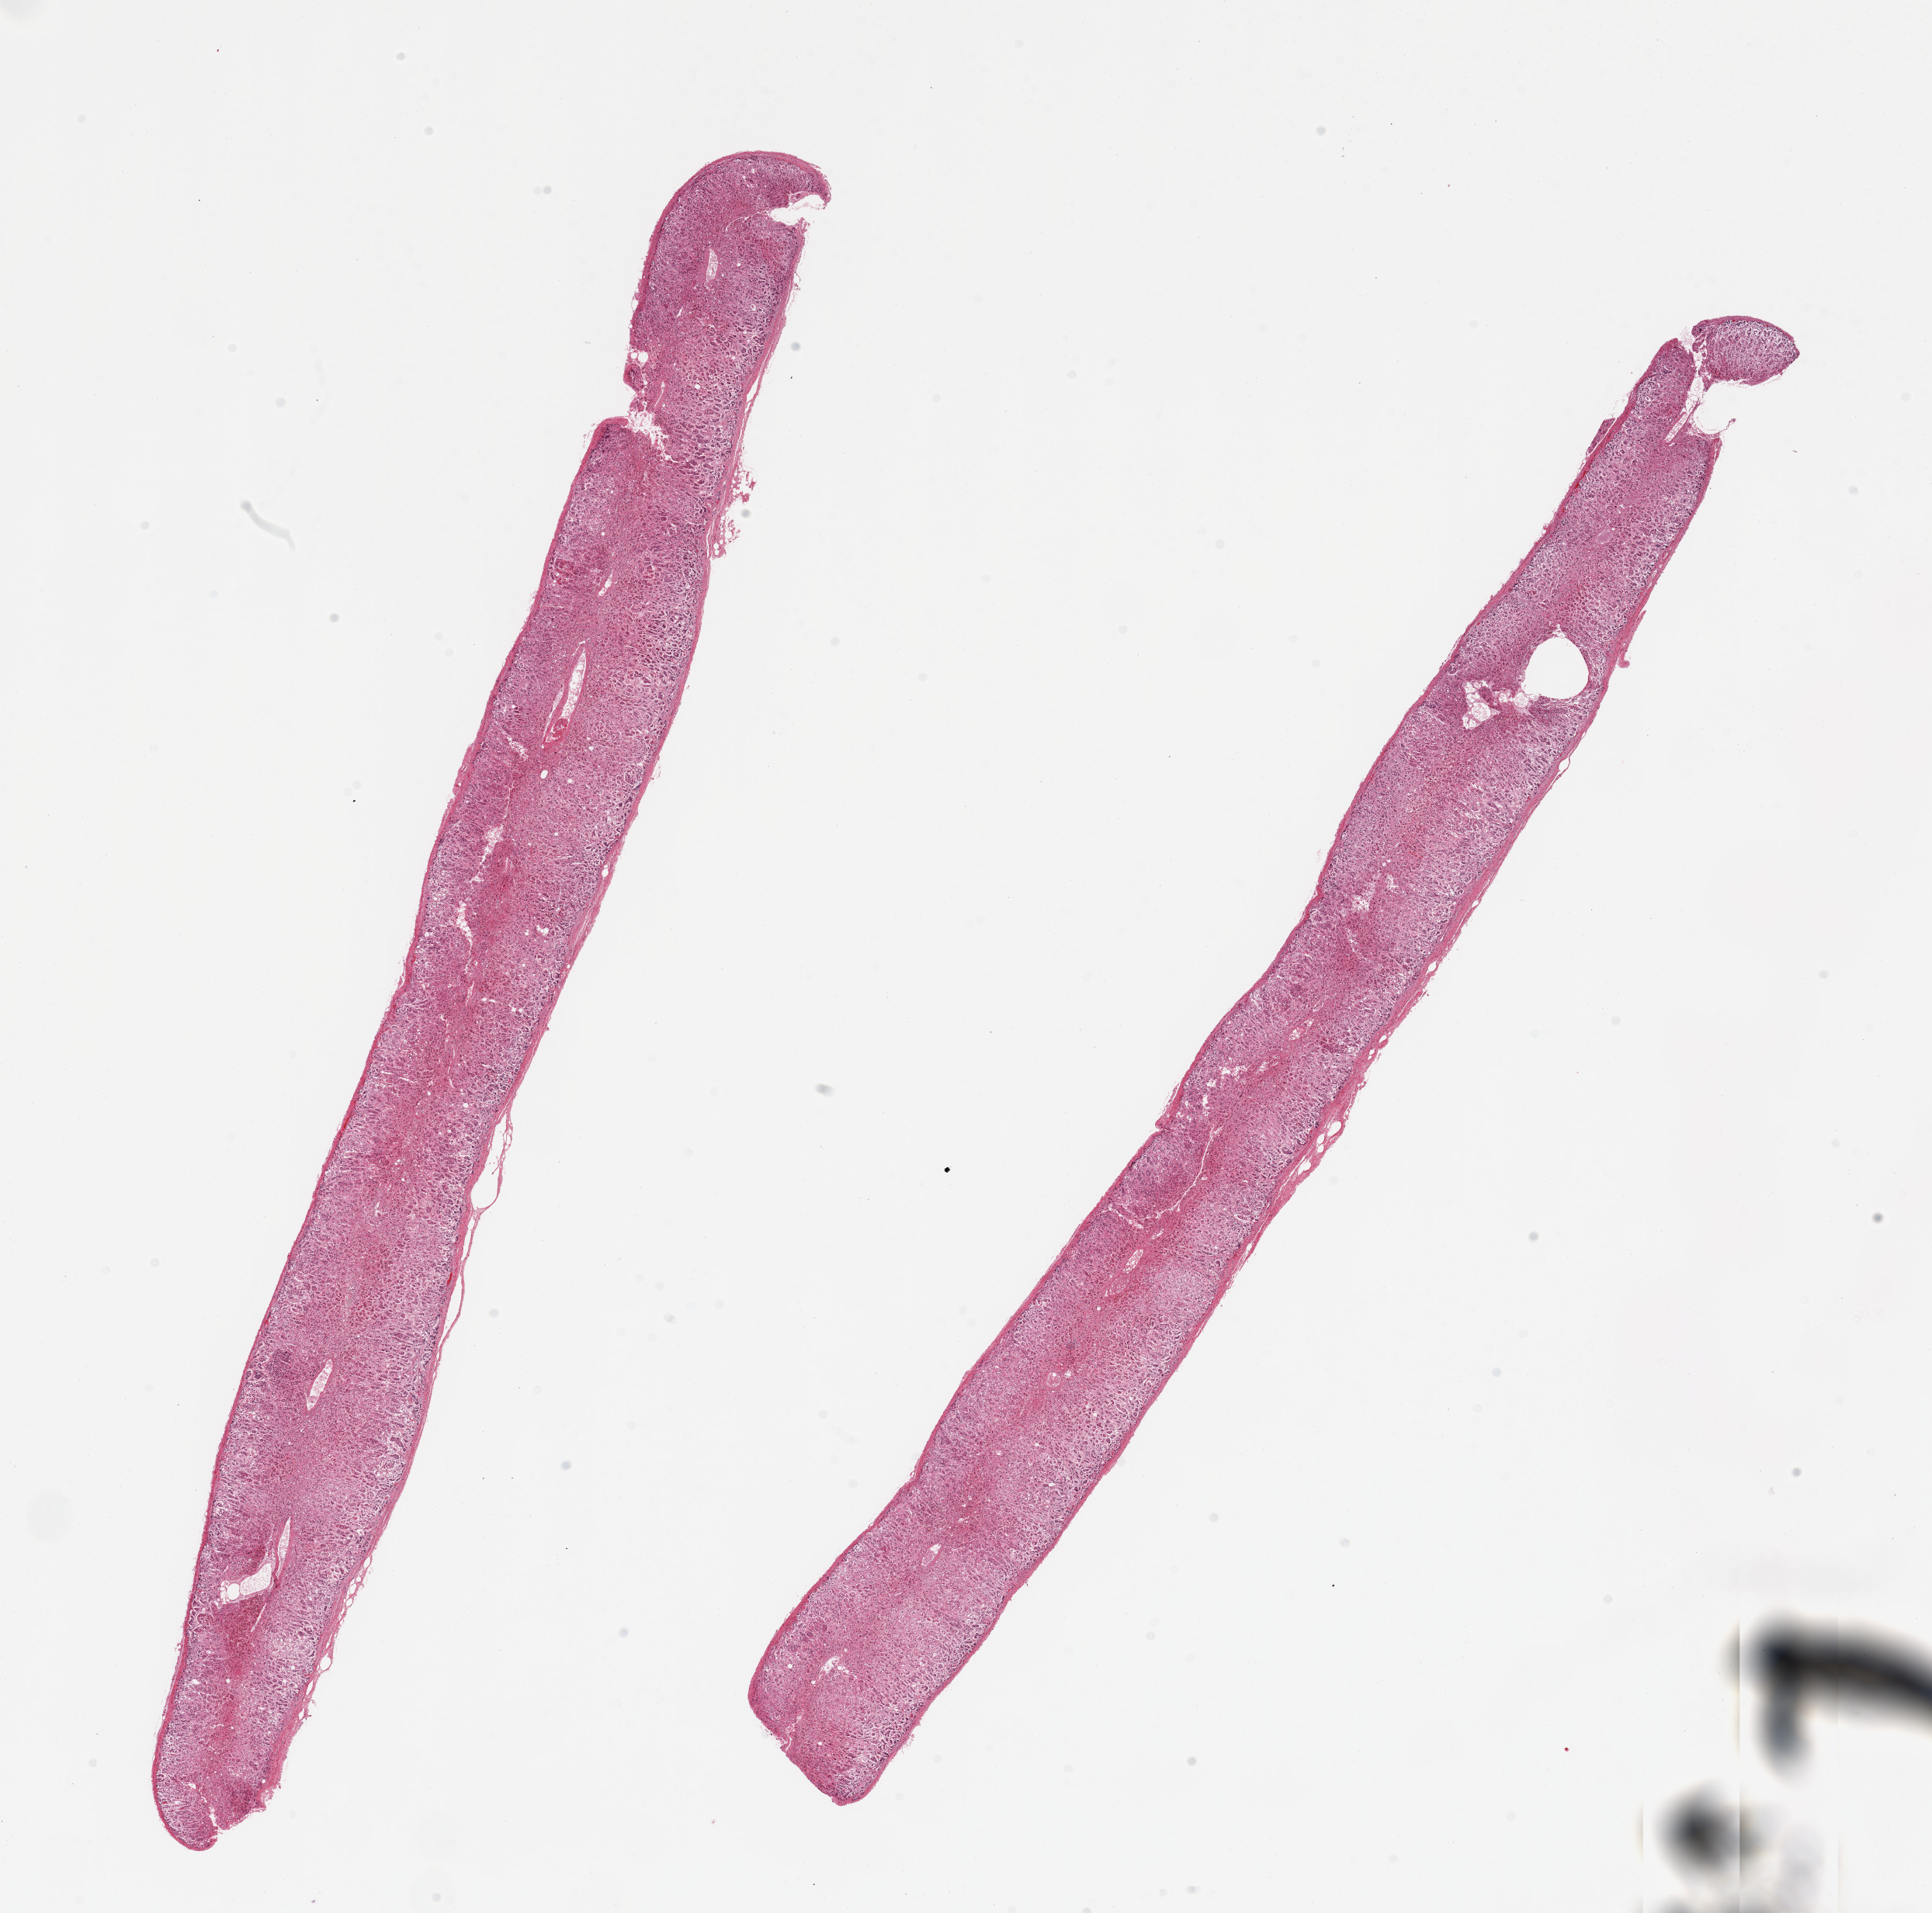
Whole-slide image, haematoxylin and eosin stain — whole scanned area (about 19.7 x 19.5 mm) shown as a low-resolution overview. PAXgene-fixed paraffin-embedded (PFPE) section. Sampled site (target tissue): adrenal gland. Tissue donor sample. Donor sex: male.
- review note (as recorded): 2 pieces, all cortex. Fairly well presreved; some areas approach score '2'